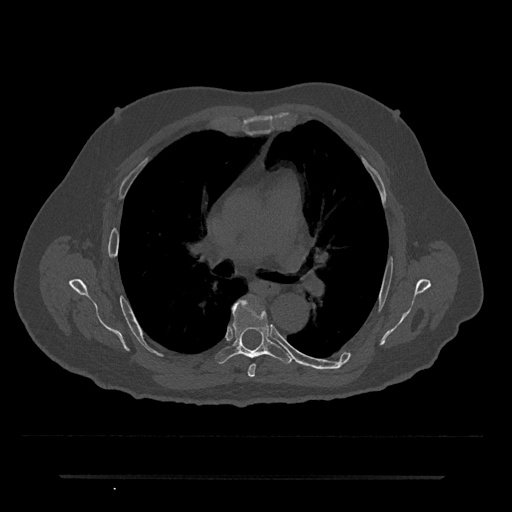
CT including the spine, one axial slice. Slice 447 of 797 in the series (ordered by position). Reconstruction kernel Br40s/3. Bone window (W 1800 / L 400 HU). 512 × 512 image matrix. Male patient, age 69 years. From the clinical record (not read from this slice): primary cancer: prostate.
Annotated regions visible in this slice (semi-automatic segmentation, software-assisted and operator-edited):
- T5 vertebra: bounding box <248,364,256,377> (left, top, right, bottom; pixels)
- T6 vertebra: <215,299,293,364>